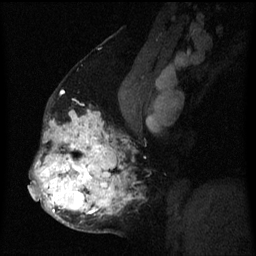
Breast MRI (dynamic contrast-enhanced), one sagittal slice; position 35 of 60 along the scan axis; dynamic contrast-enhanced series, image 2 of 3 at this slice position (ordered by acquisition); 1.5 T; TE 4.2 ms, TR 8 ms; 2 mm slice thickness; 256 × 256 image matrix, field of view 190 × 190 mm. Patient: female, 50 years.
Outlined on this slice (semi-automatically segmented with operator editing):
- analysis volume of interest (the breast-tissue region the enhancement analysis was run in; not a lesion): bounding box [x1, y1, x2, y2] px = [32, 110, 137, 233]
- tumour enhancement mask (voxels above the 70 % enhancement threshold inside the analysis volume of interest): [32, 110, 130, 219]